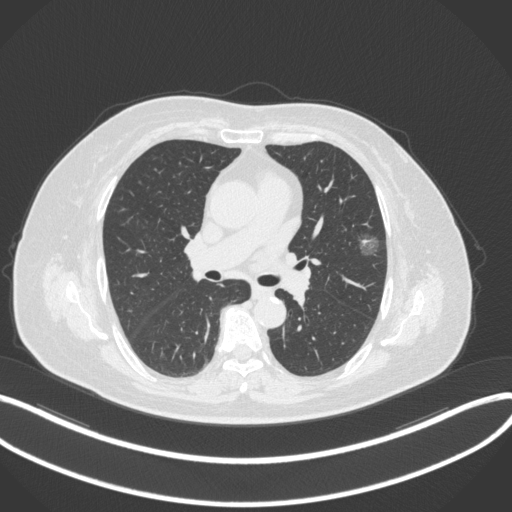
Chest CT, one axial slice. Position 179 of 286 along the scan axis. Reconstruction kernel B31f. Lung window (W 1500 / L -600 HU). 1 mm slice thickness. 512 × 512 image matrix, field of view 400 × 400 mm. Patient: female, 76 years. From the clinical record (not read from this slice): clinical TNM (as recorded): T1b N0 M0; histopathological grade: G1-2.
Outlined on this slice (bounding box drawn by a radiologist):
- lung tumour (recorded histology: adenocarcinoma): bounding box [x1, y1, x2, y2] px = [355, 226, 383, 263]